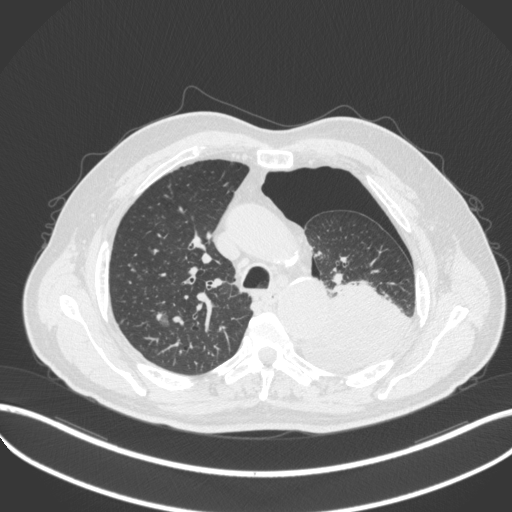
Chest CT, one axial slice. Slice 363 of 466 in the series (ordered by position). Reconstruction kernel B31f. 120 kVp. Lung window (W 1500 / L -600 HU). 512 × 512 image matrix, field of view 400 × 400 mm. Patient: male, 76 years. From the clinical record (not read from this slice): clinical TNM (as recorded): T3 N0 M1b.
Annotated regions visible in this slice (rectangle marked by the reading radiologist):
- lung tumour (recorded histology: adenocarcinoma): bounding box (x1, y1, x2, y2) in pixels: (297, 276, 415, 374)